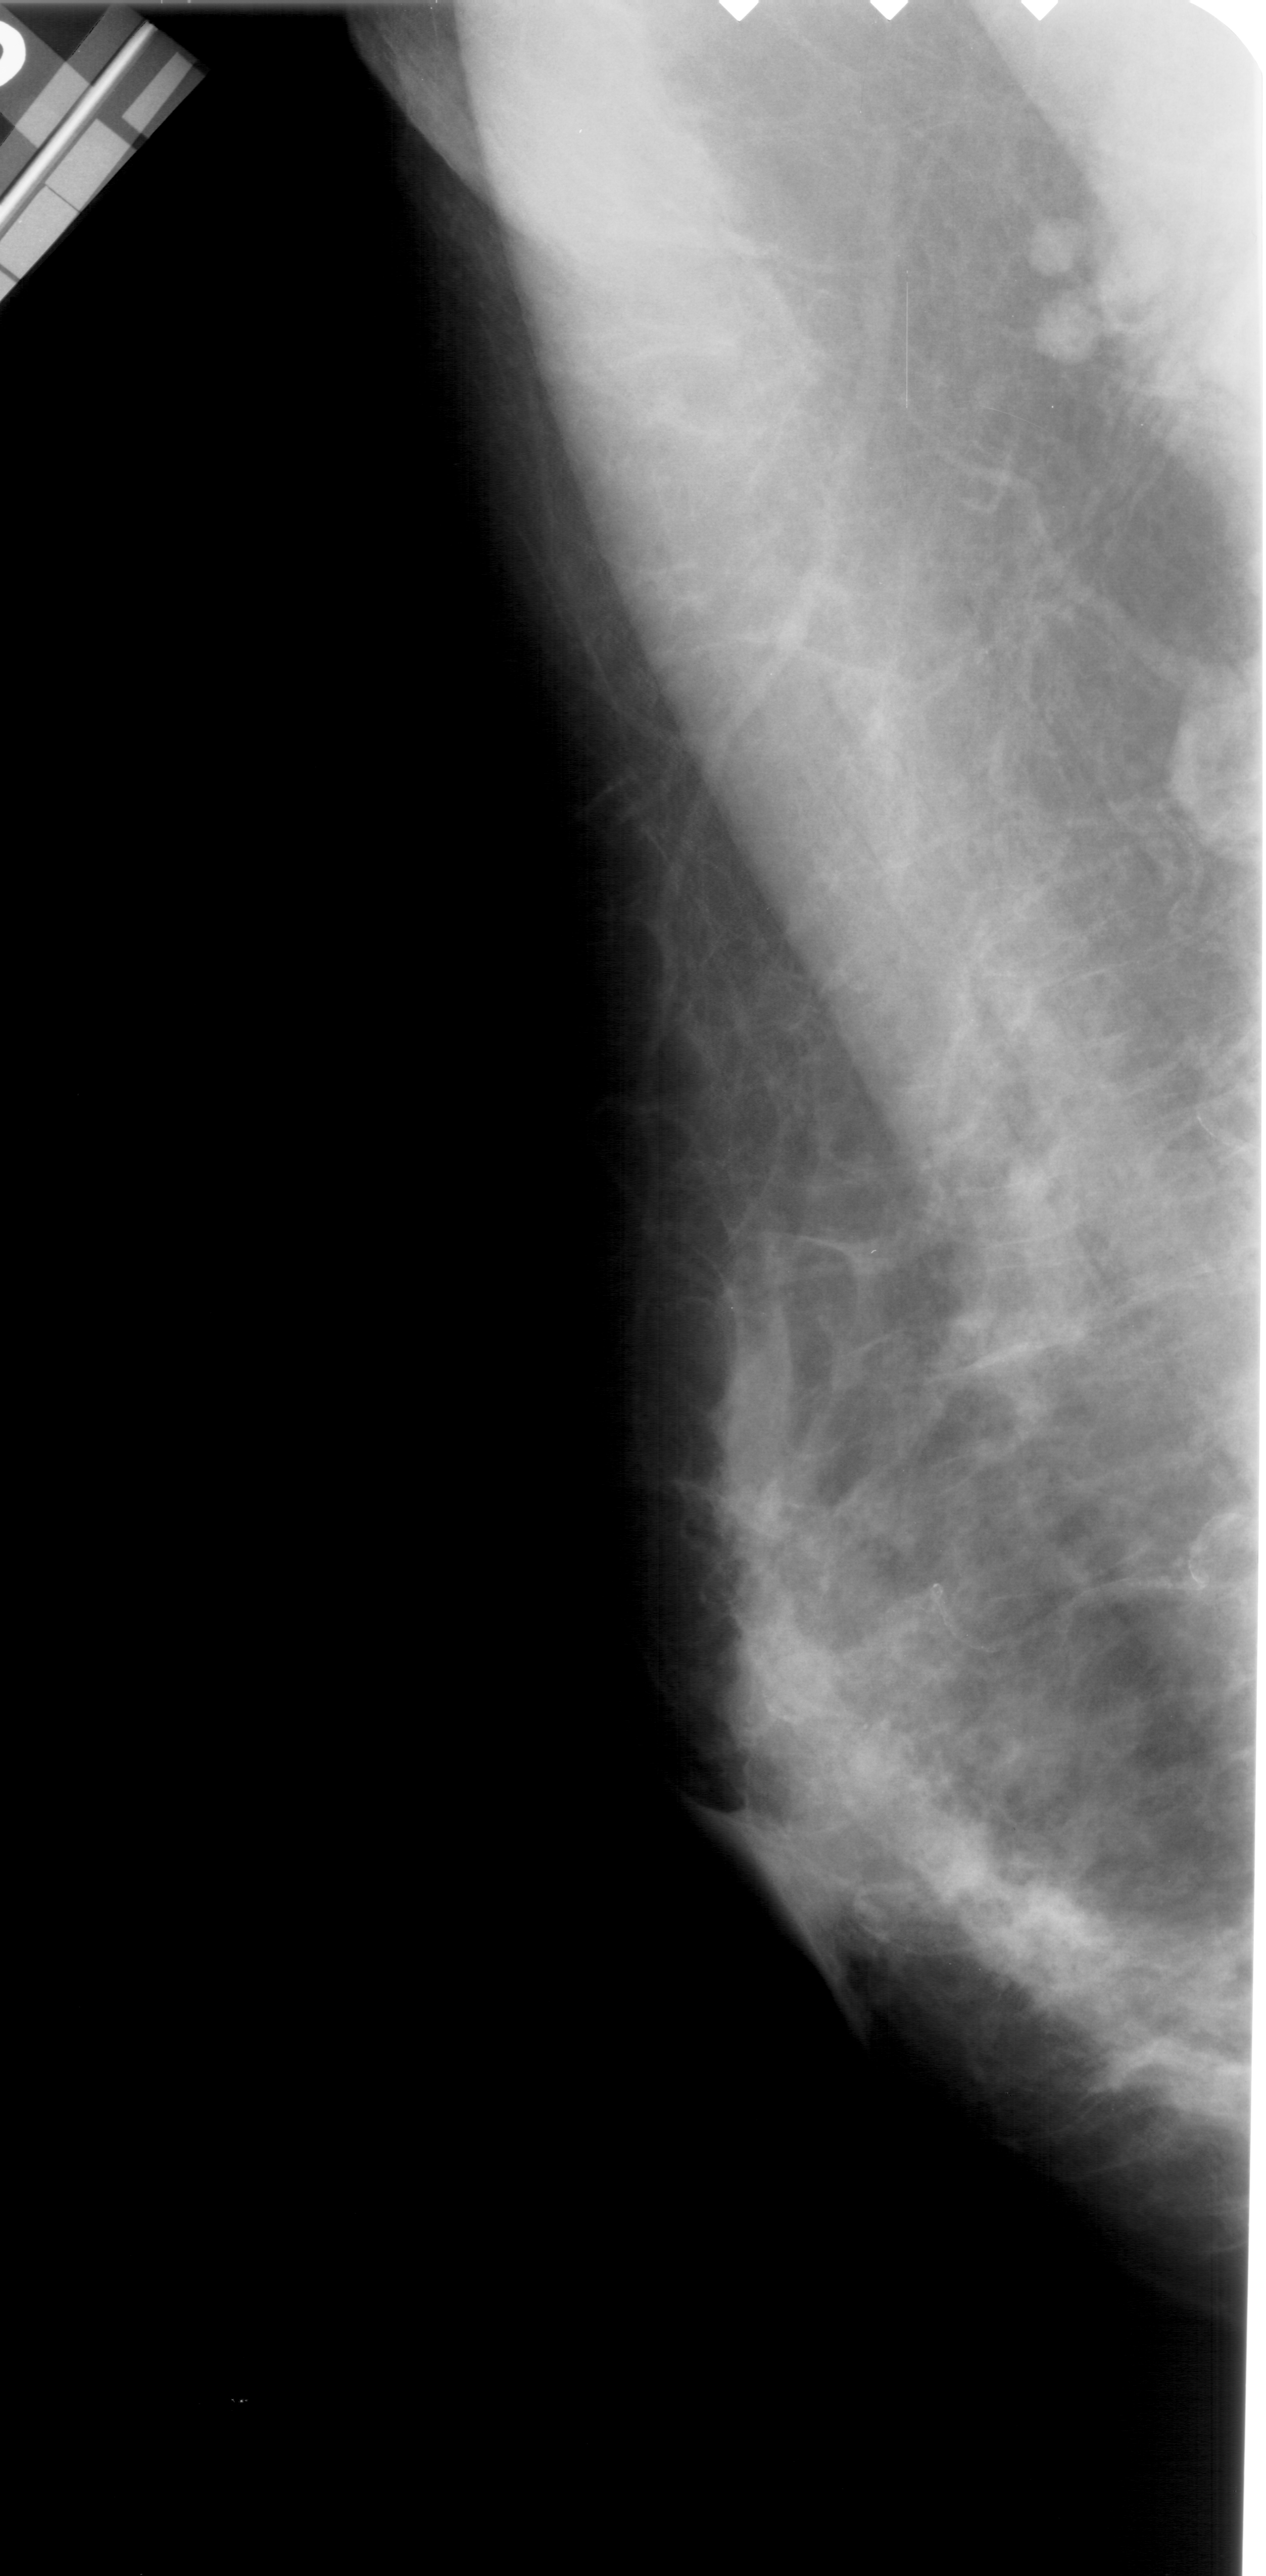
Digitized screen-film mammogram; left breast; mediolateral oblique (MLO) view; breast composition: extremely dense (BI-RADS density category 4 of 4).
Marked abnormality: mass, shape irregular, margins spiculated; BI-RADS assessment category 5; pathology result (as recorded, not read from the image): benign.